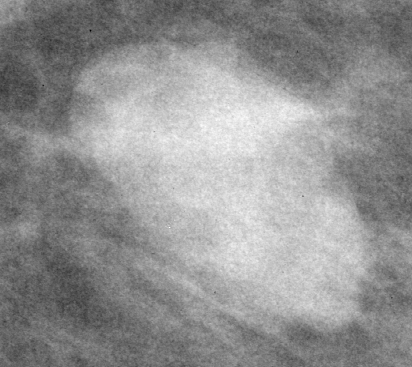
Crop from a digitized film mammogram around one marked abnormality; left breast; MLO view; BI-RADS breast density category 2 (scale 1–4).
Mass, shape lobulated / oval, margins circumscribed; BI-RADS assessment category 4; subtlety rating 5 on a 1 (subtle) to 5 (obvious) scale; pathology (as recorded): benign.